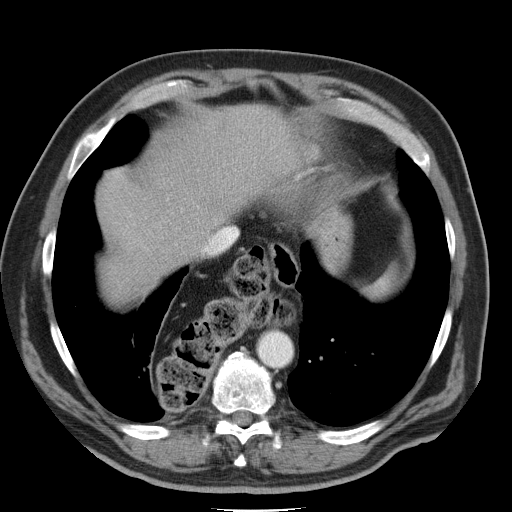
Contrast-enhanced abdominal CT, one axial slice; slice 40 of 45 in the series (ordered by position); intravenous contrast given; soft-tissue window (W 400 / L 40 HU); 5 mm slice thickness; 512 × 512 image matrix, field of view 386 × 386 mm. Male patient, age 65 years. Case-level facts recorded for this patient, not image findings: diagnosis: colorectal cancer liver metastases, imaged before liver resection; multiple liver metastases: yes; largest metastasis: 4.9 cm; disease in both lobes: no.
Annotated regions visible in this slice (expert manual segmentation):
- hepatic veins: box from (x=204, y=227) to (x=233, y=253) px
- liver: (x=100, y=107)–(x=293, y=299)
- planned liver remnant (the part of the liver to remain after resection): (x=143, y=108)–(x=293, y=243)
- portal vein (with intrahepatic branches): (x=126, y=214)–(x=135, y=228)